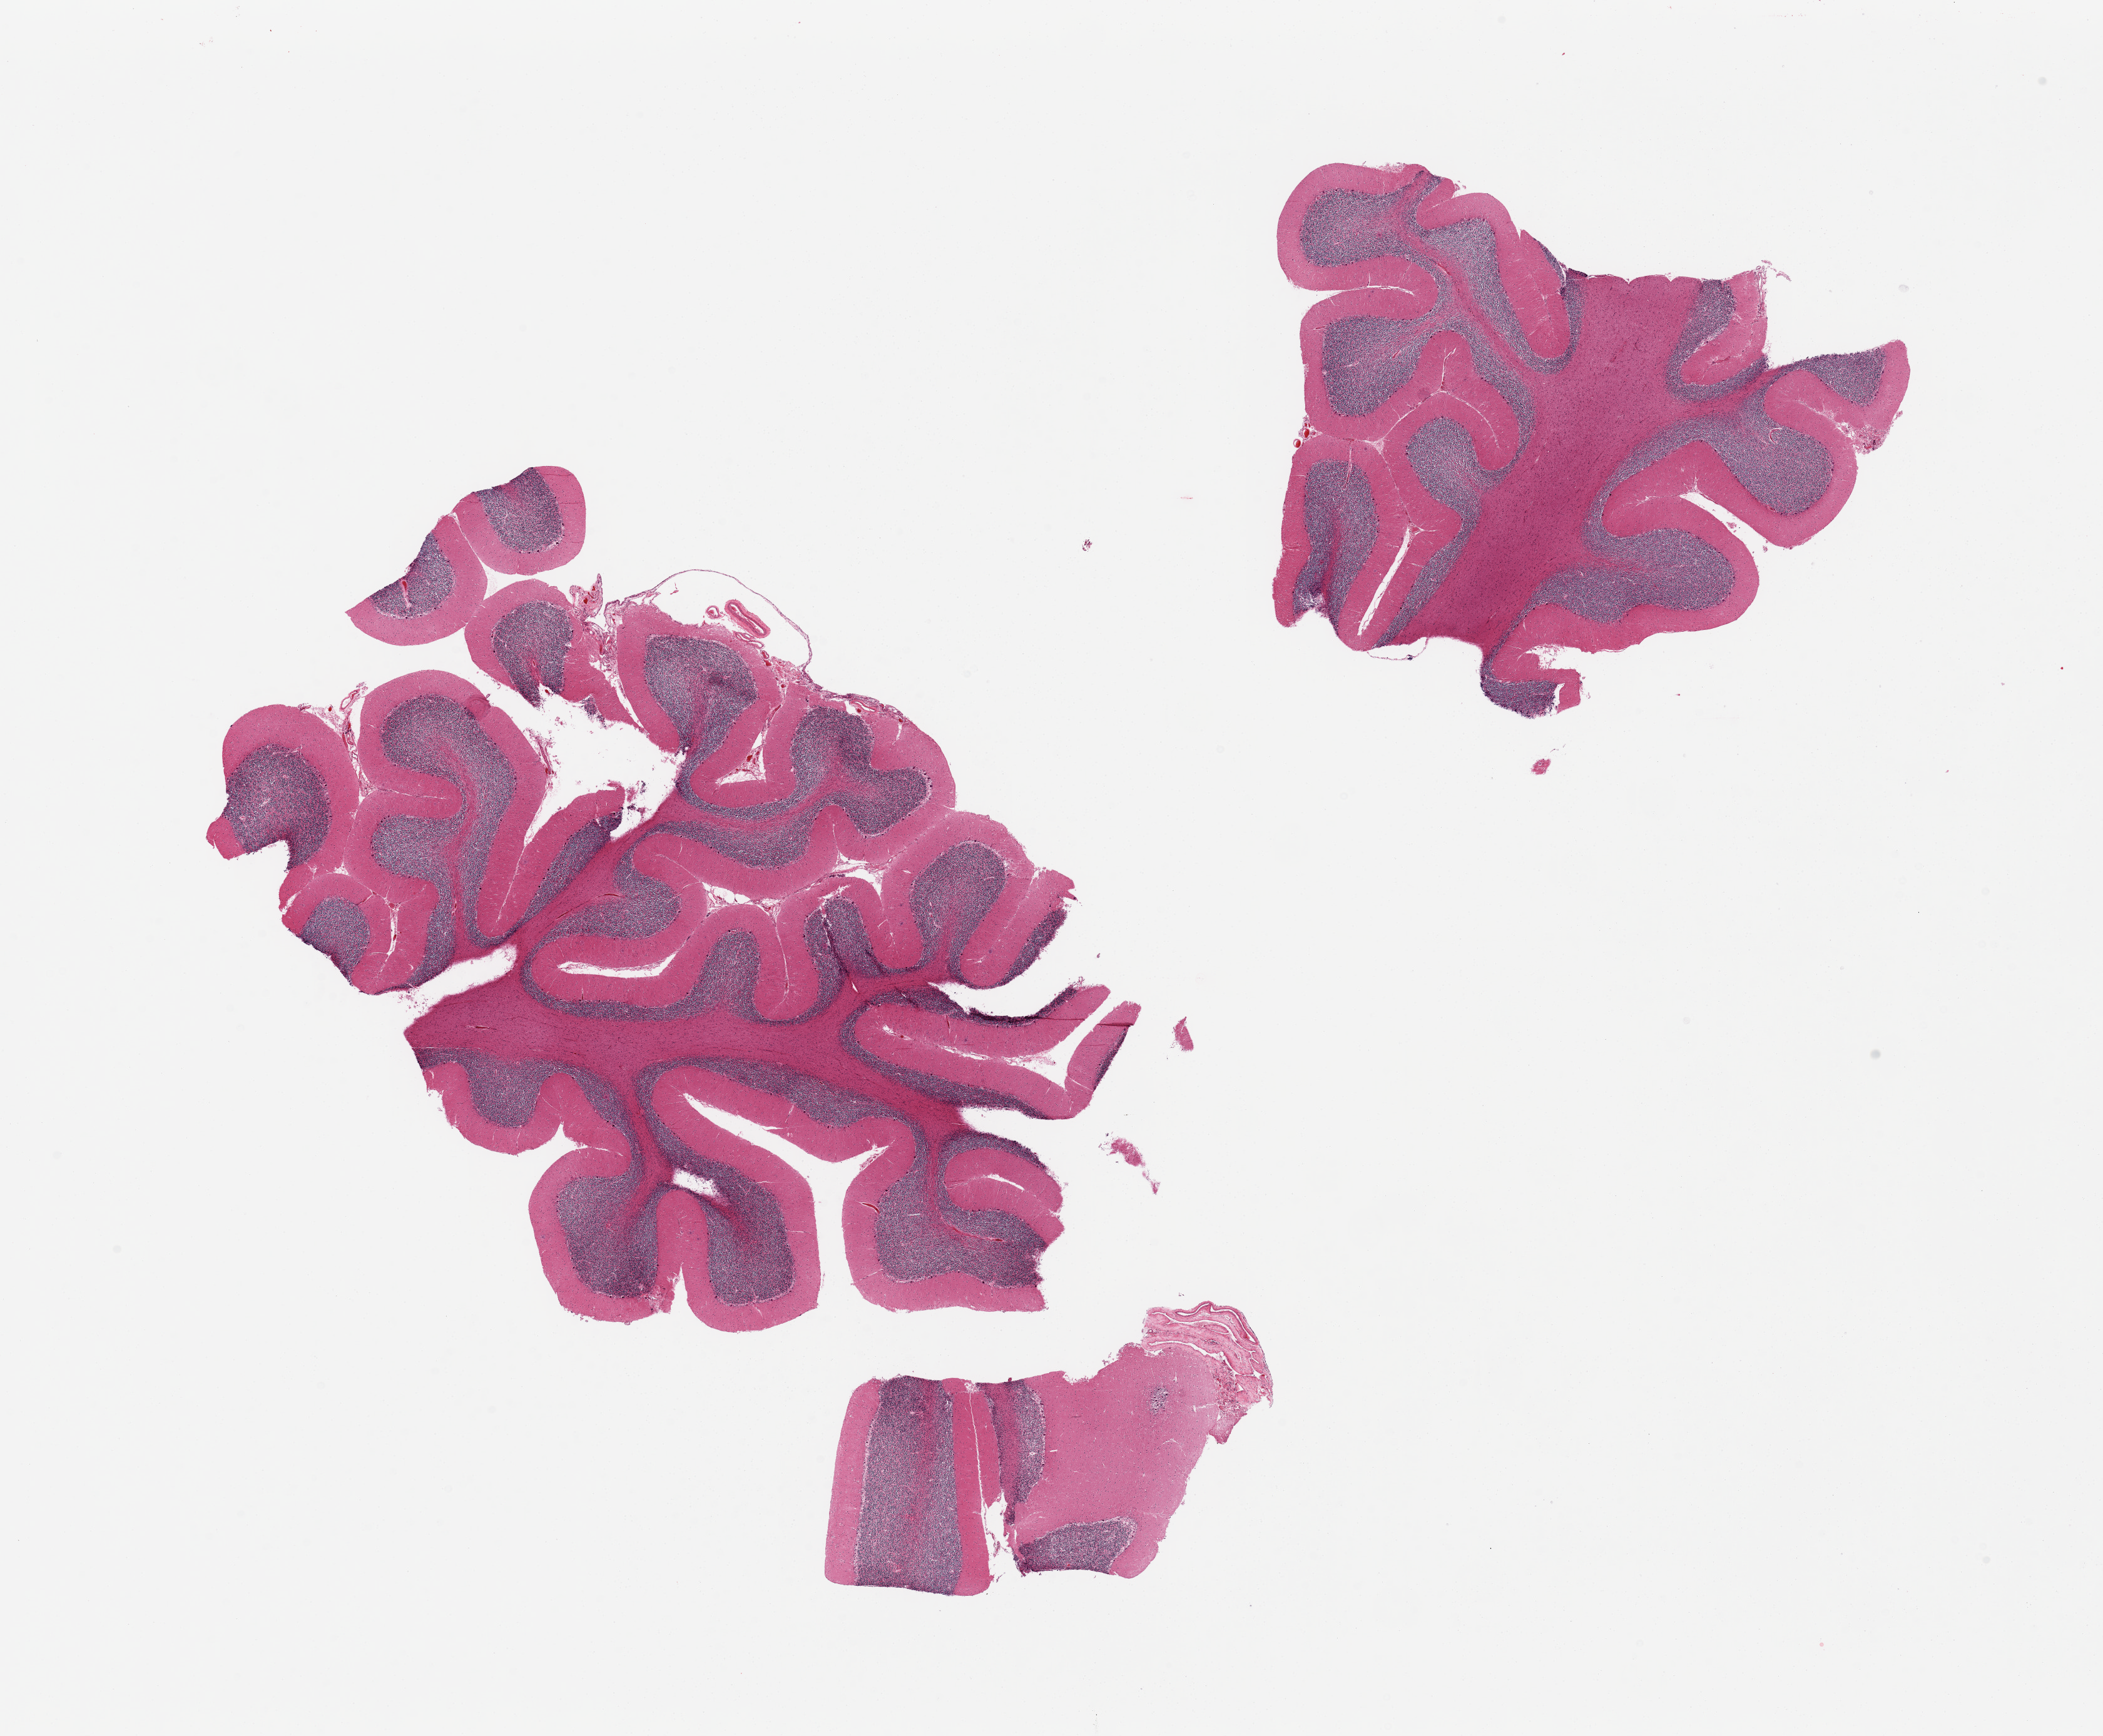
Whole-slide image, hematoxylin and eosin (H&E) stain, brightfield, low-resolution overview of the scanned area, about 26.6 x 21.9 mm (slide scanned at 20x). PAXgene-fixed, paraffin-embedded tissue. Target tissue: cerebellum. Tissue donor sample. Male donor.
• review note (as recorded): 2 pieces, Purkinje cells layer seen, corpora amylacea seen